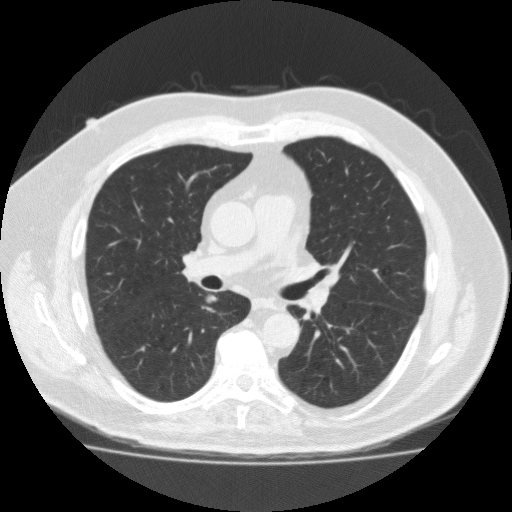
Low-dose screening chest CT, one axial slice. Slice 110 of 183 in the series (ordered by position). Reconstruction kernel FC10. 120 kVp. Lung window (W 1500 / L -600 HU). 2 mm slice thickness. 512 × 512 image matrix, field of view 391 × 391 mm.
Outlined on this slice (outlined manually by an expert reader):
- lesion 1 (tumor, lower lobe of right lung): bounding box (x1, y1, x2, y2) in pixels: (208, 296, 216, 301)